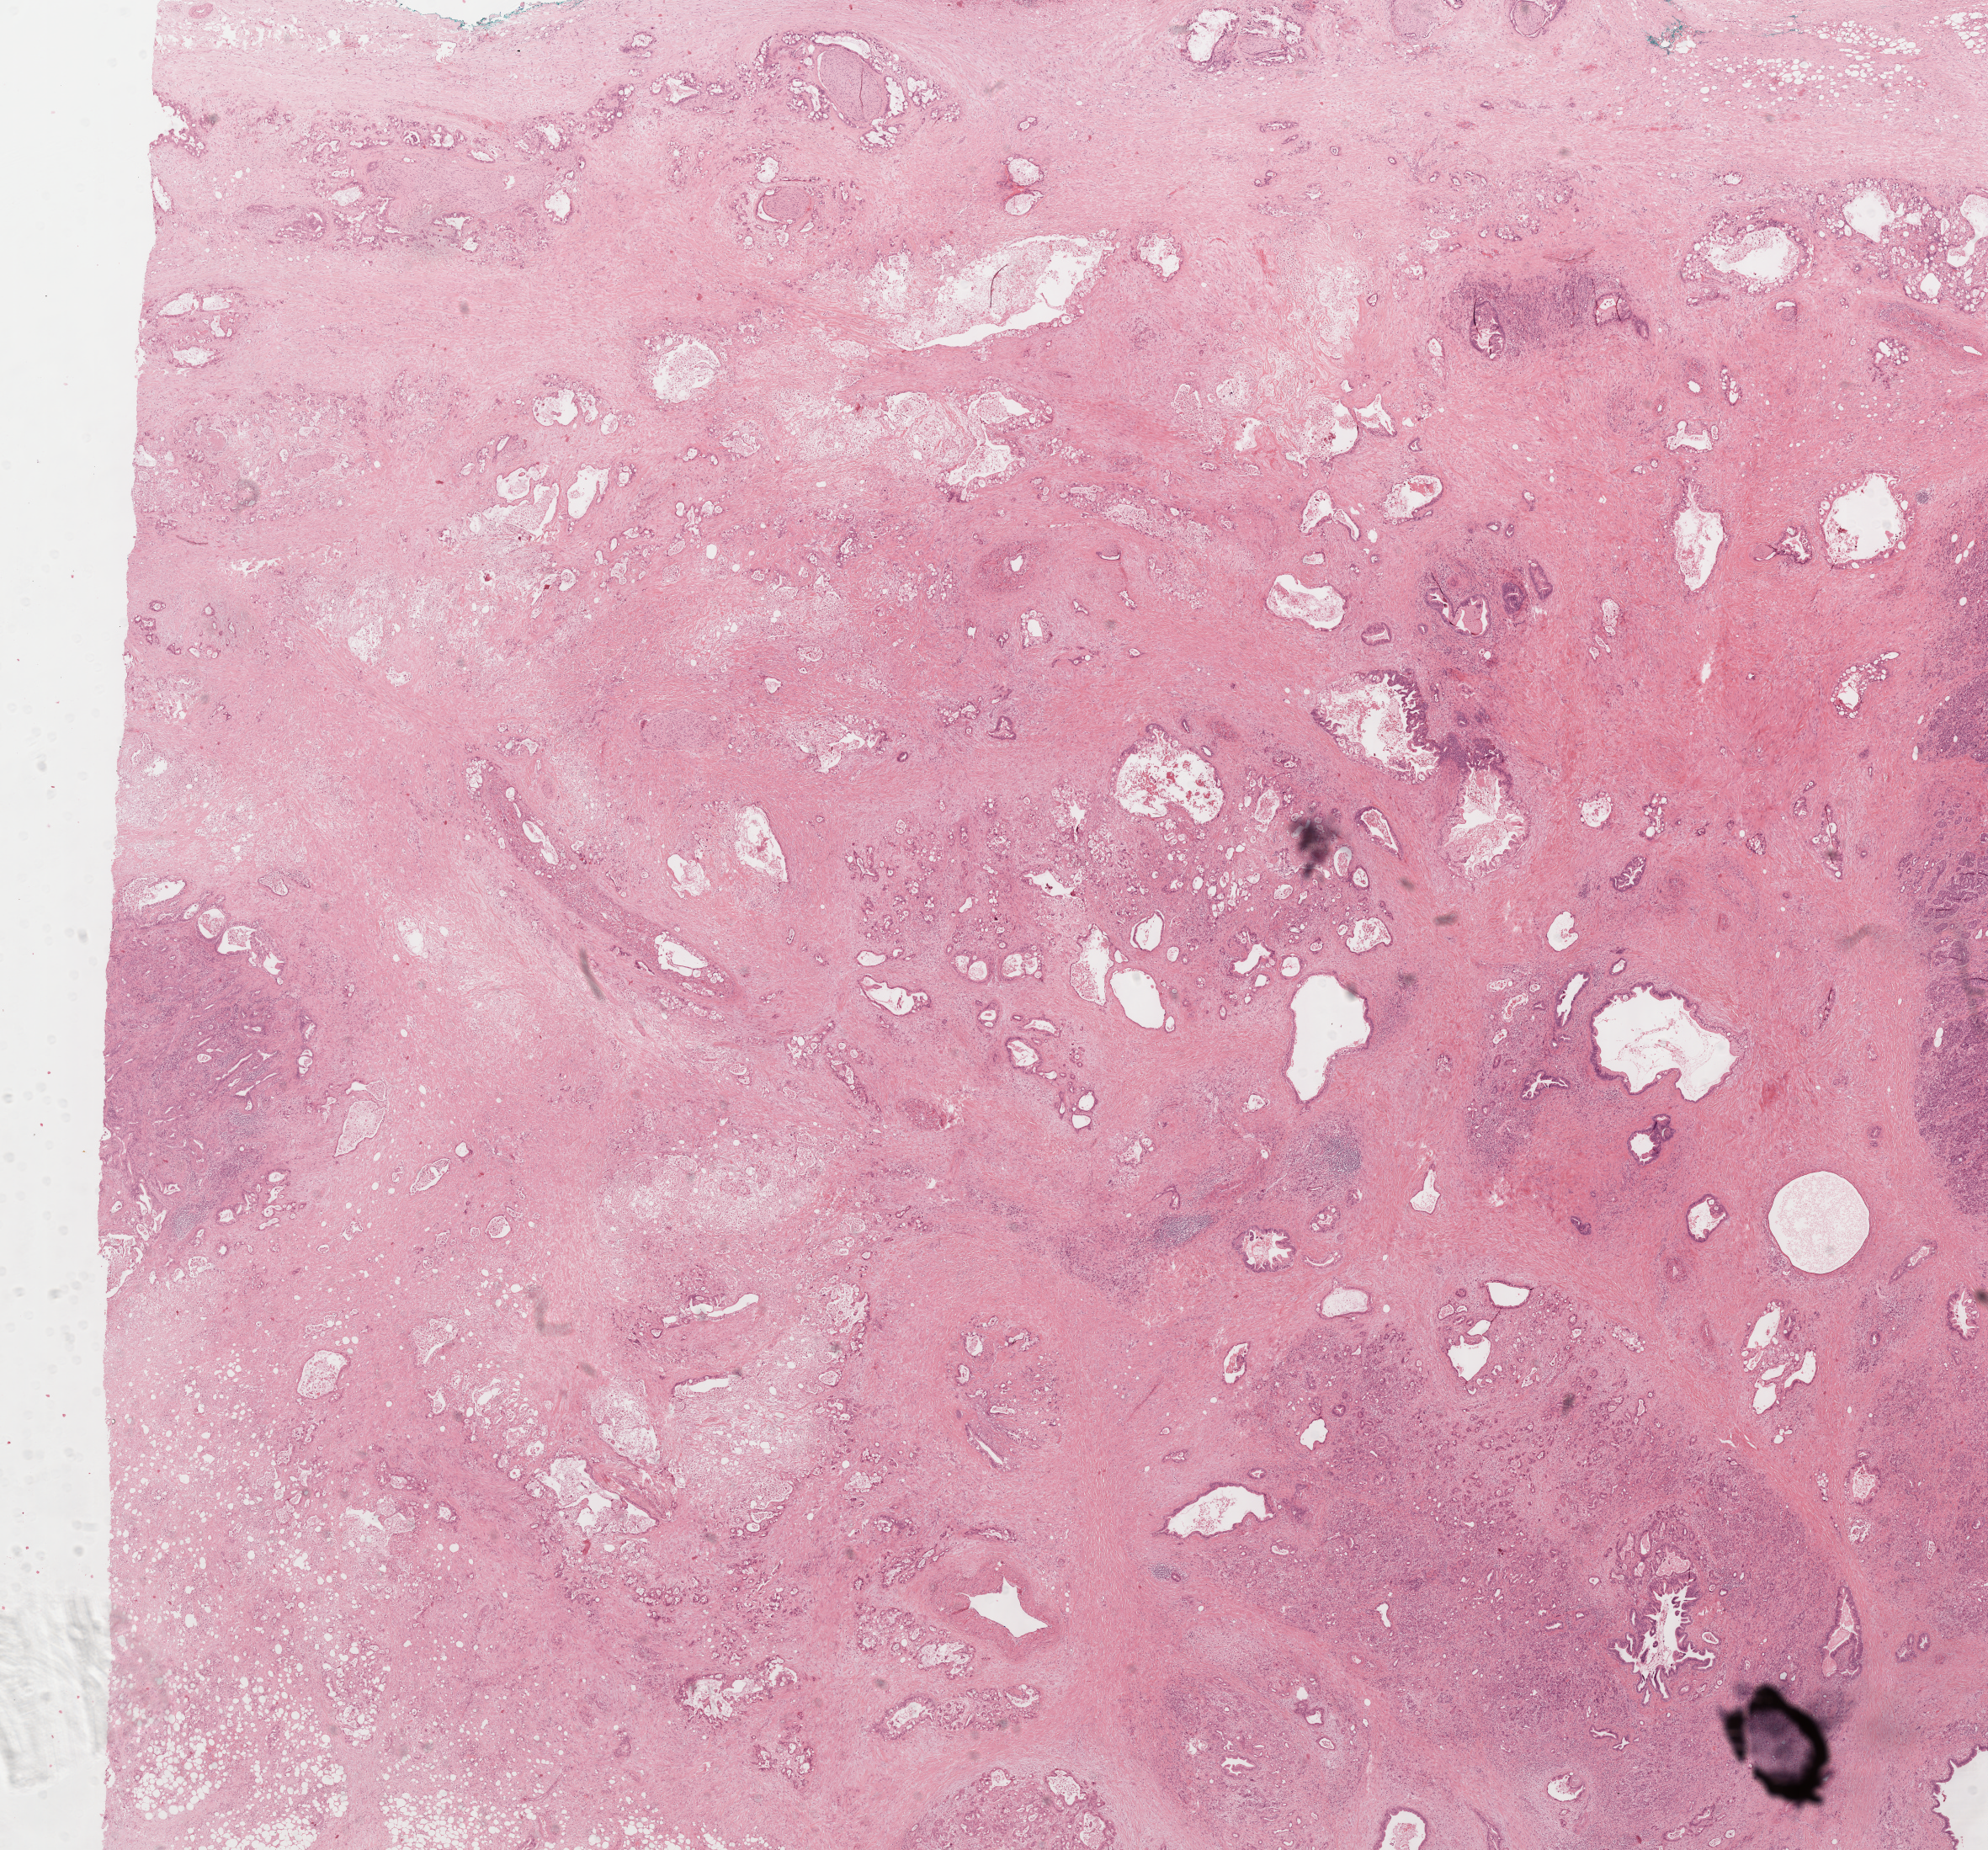
H&E-stained whole-slide image — a low-resolution overview of the entire scanned area, about 18.8 x 17.5 mm; formalin-fixed paraffin-embedded (FFPE) diagnostic section; pancreas, primary tumour sample. Male, age 66 years at initial diagnosis. Histologic grade: G3 (poorly differentiated).
Pathologic diagnosis: Infiltrating duct carcinoma, NOS (head of pancreas). AJCC pathologic stage: IIB. Lymph nodes positive (case pathology): 6 of 19 examined.